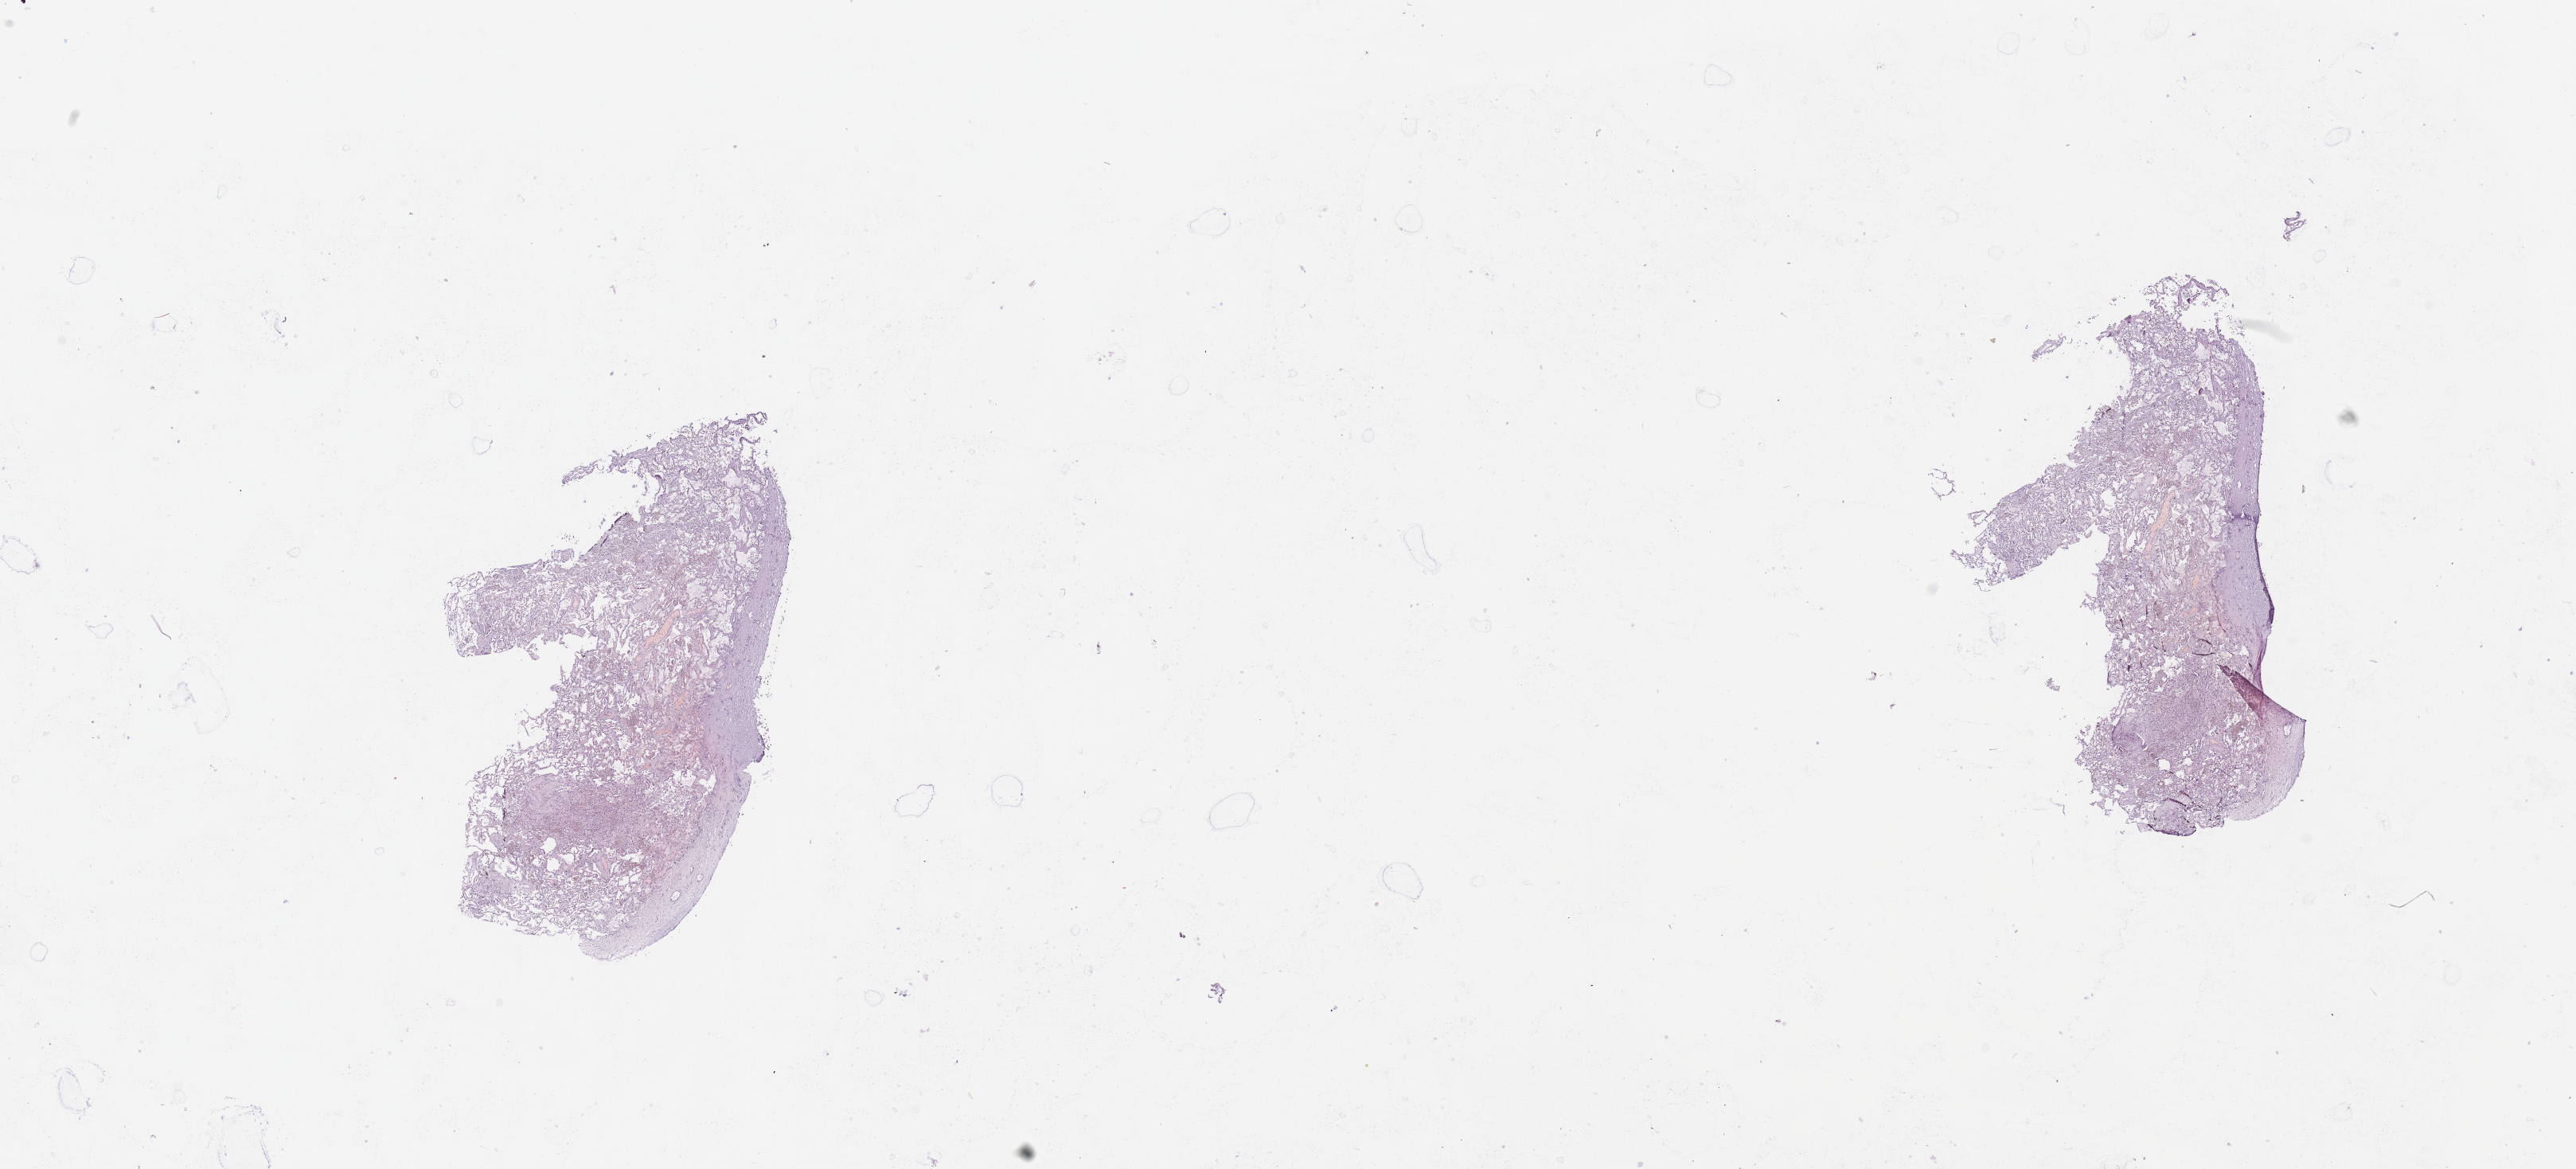
Whole-slide histology image, H&E-stained, a low-resolution overview of the entire scanned area, about 25.6 x 11.6 mm. Normal (non-tumour) tissue sample, sampled site: lung. Patient: male, age 51 years.
- this section: normal (non-tumour) tissue from the same patient
- patient diagnosis: Squamous cell carcinoma, NOS